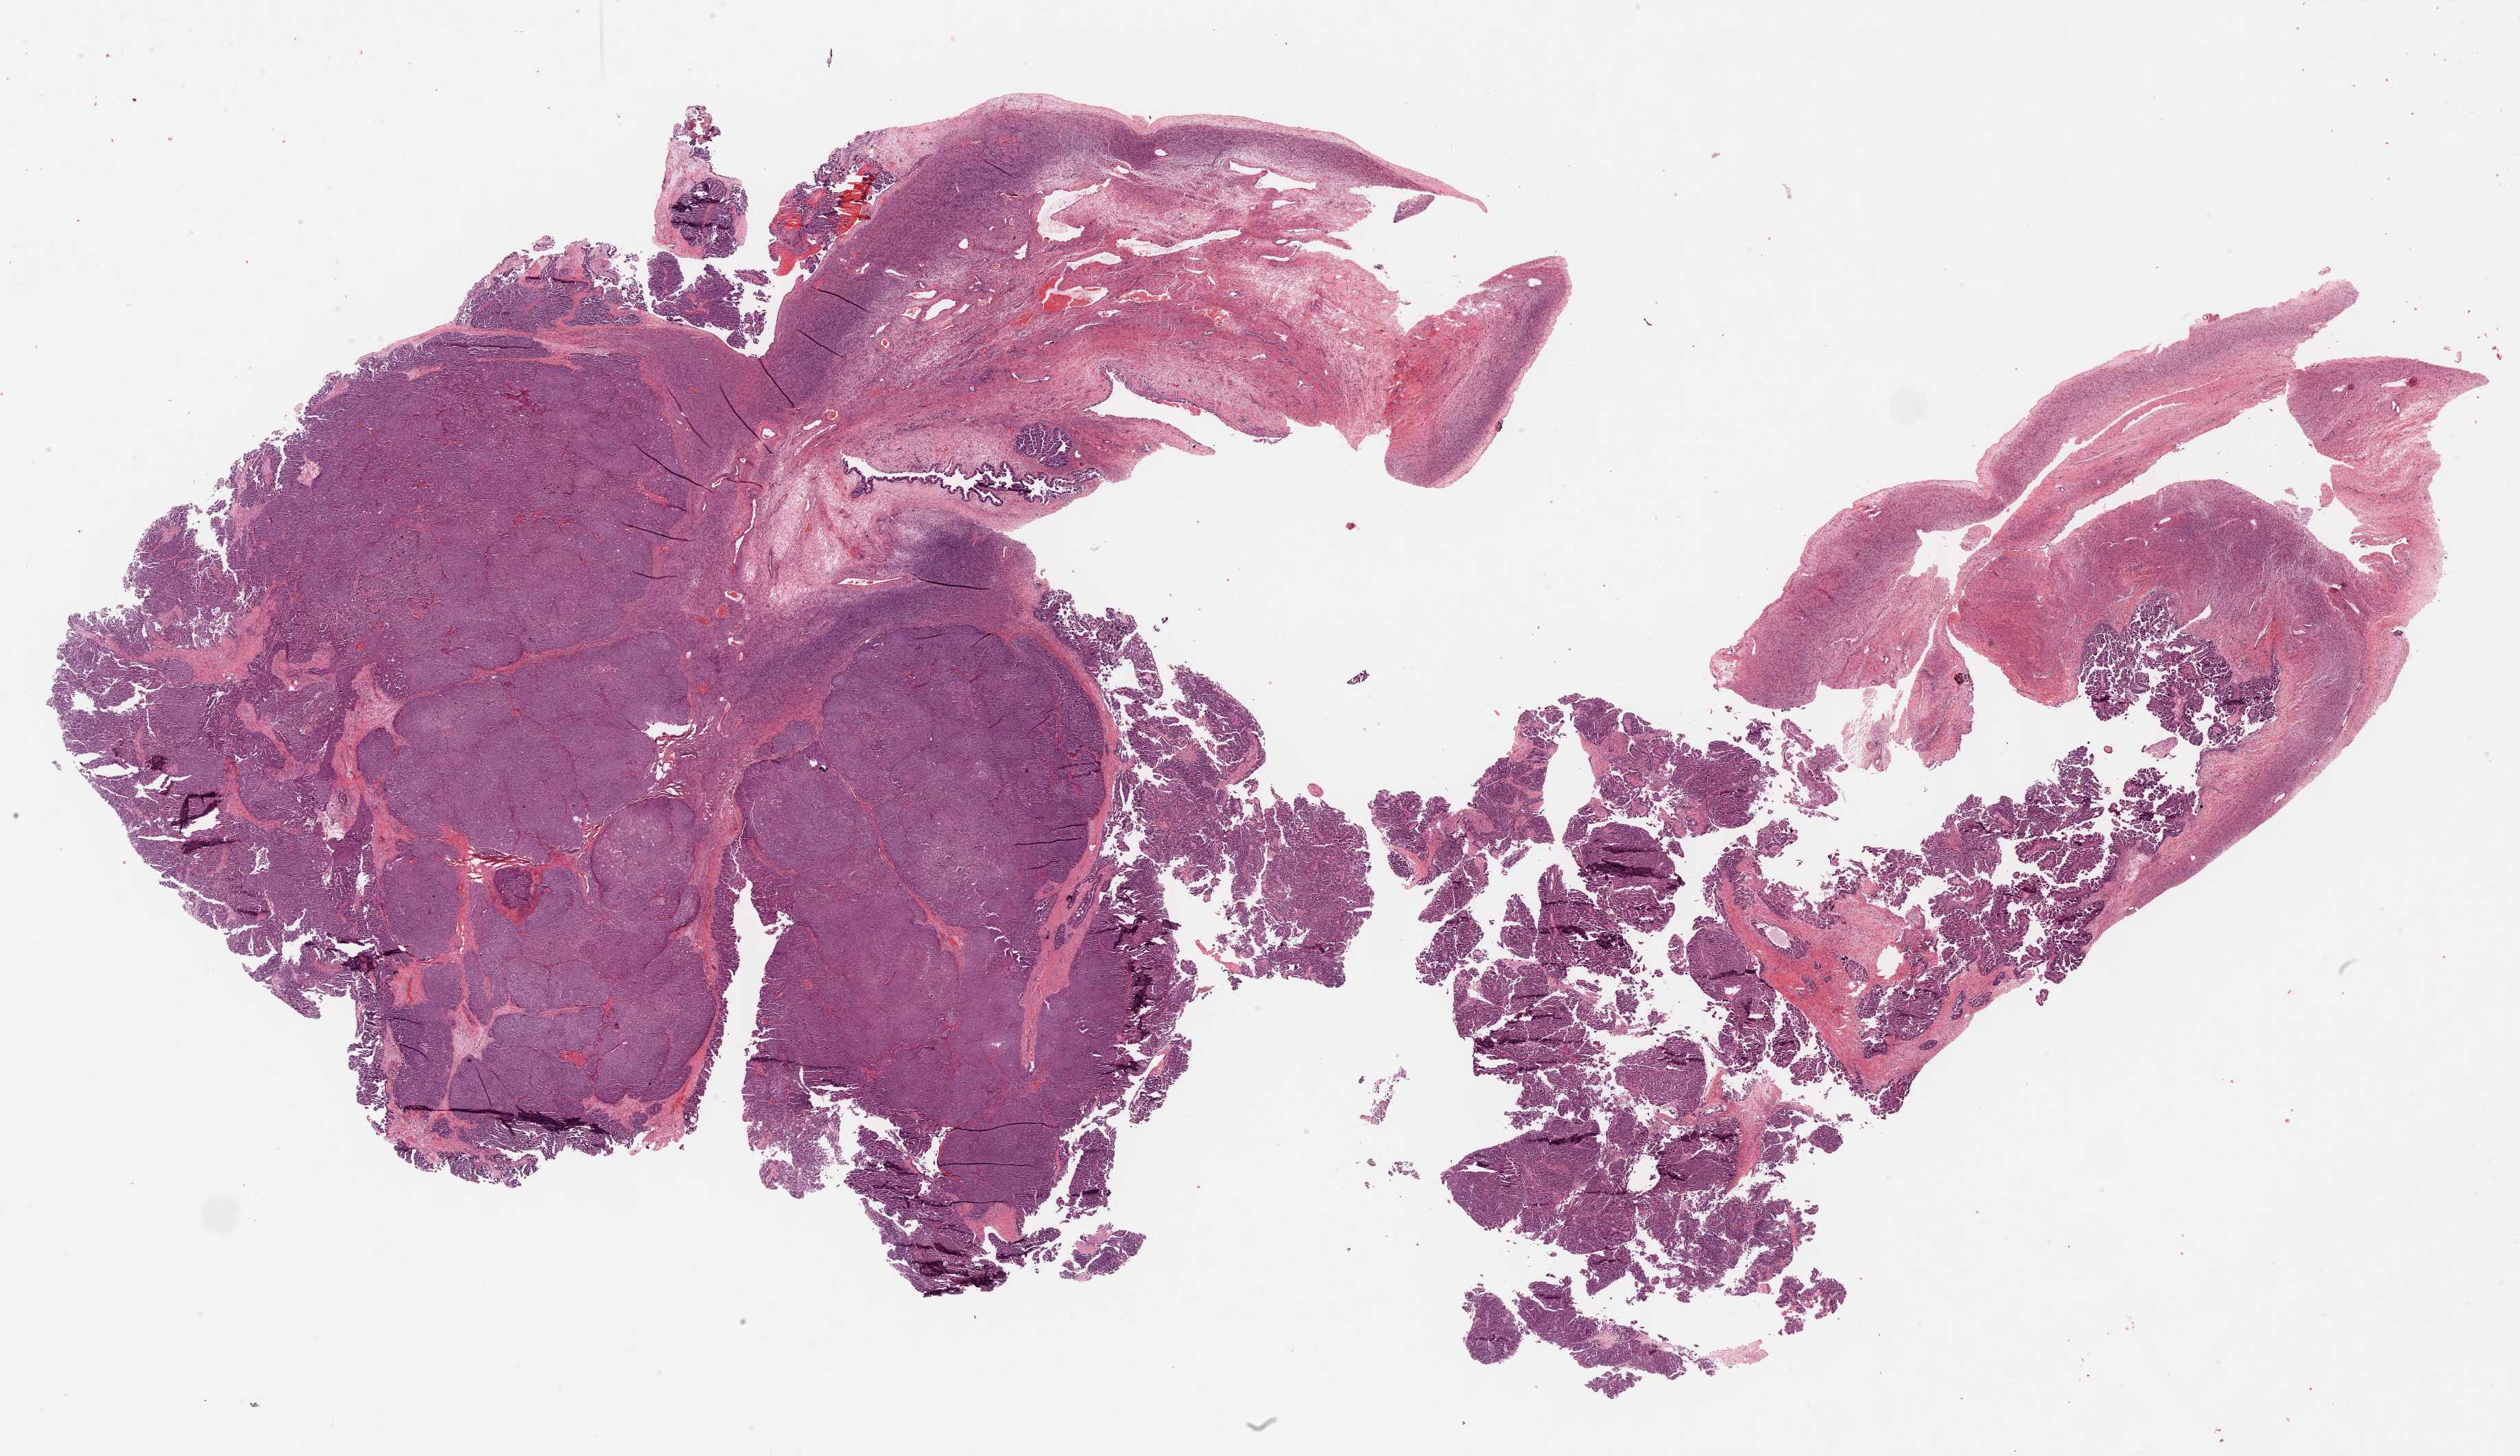
H&E whole-slide image — a low-resolution overview of the entire scanned area, about 29.7 x 17.1 mm (slide scanned at 40x), FFPE section, primary tumour sample from the ovary. Female, age 59 years at initial diagnosis. Histologic grade: G3 (poorly differentiated).
* FIGO stage: IV
* laterality: bilateral
* diagnosis: Serous cystadenocarcinoma, NOS